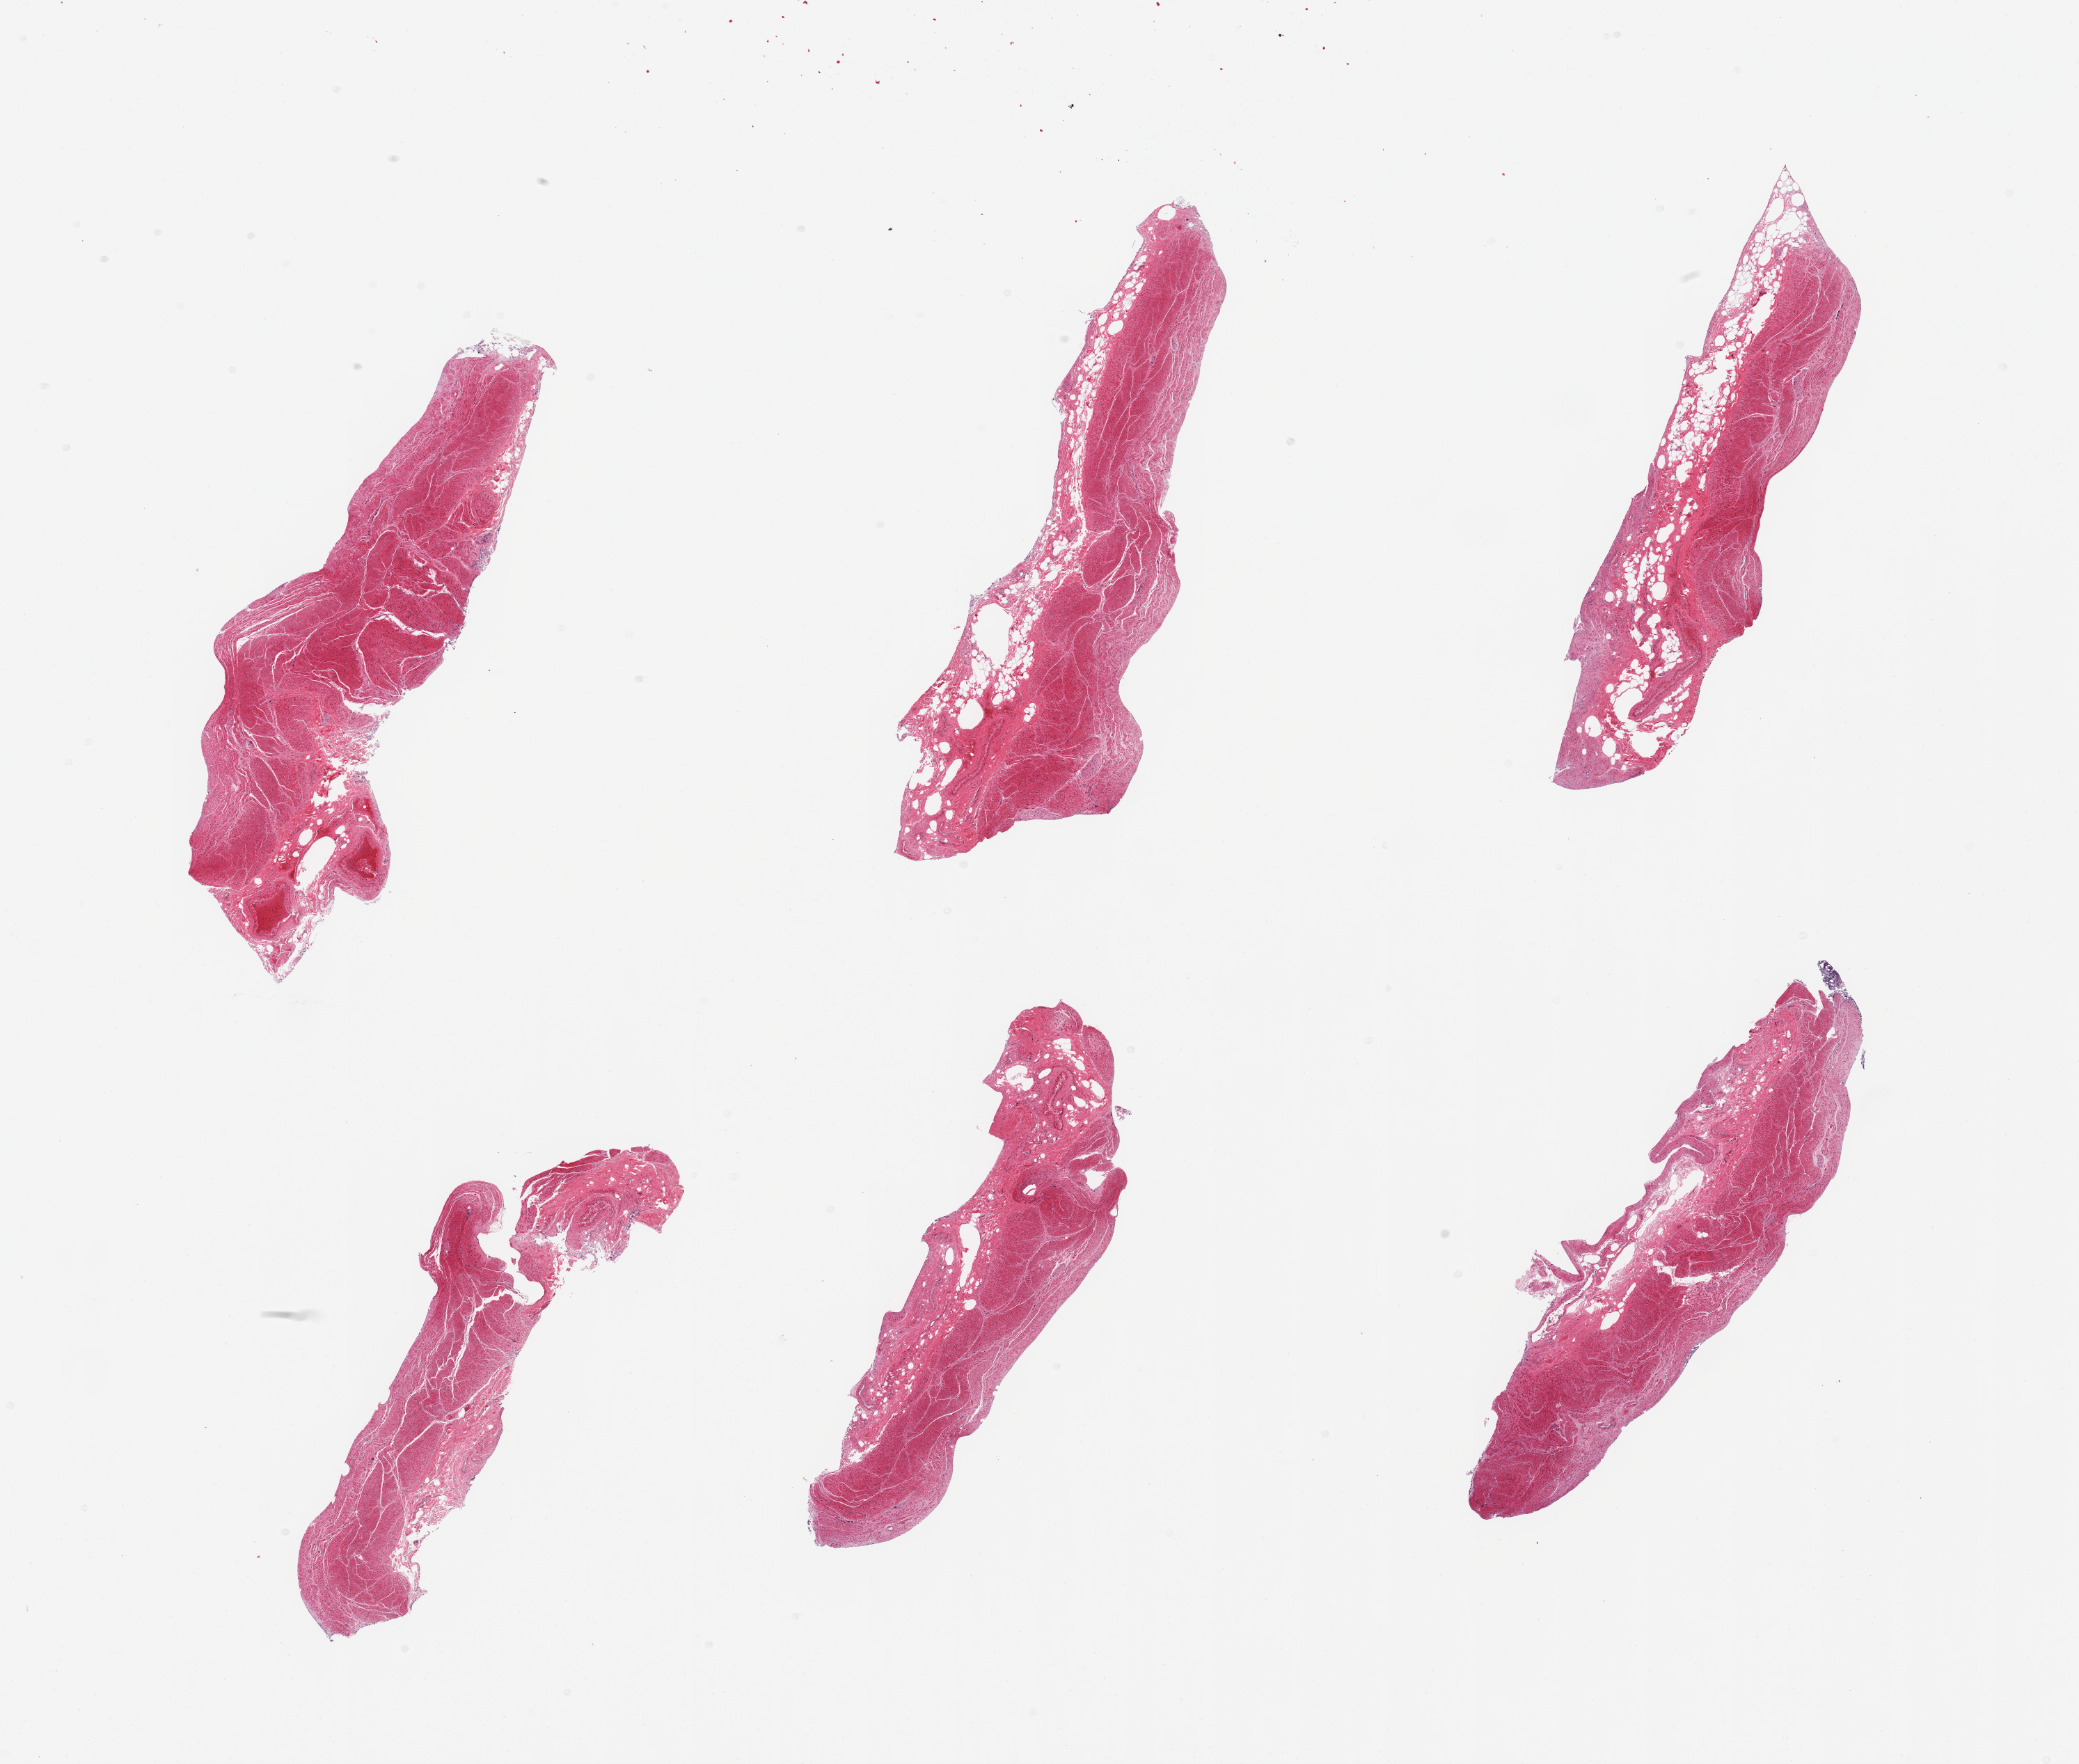
Digitized H&E-stained section — low-resolution overview of the scanned area, about 23.6 x 20.0 mm (from a 20x scan). PAXgene-fixed paraffin-embedded (PFPE) section. Sampled site (target tissue): stomach. Tissue donor sample. Donor sex: male.
Pathologist's review note for this sample: 6 pieces; muscularis, only tiny focus of totally autolyzed residual gastric mucosa.